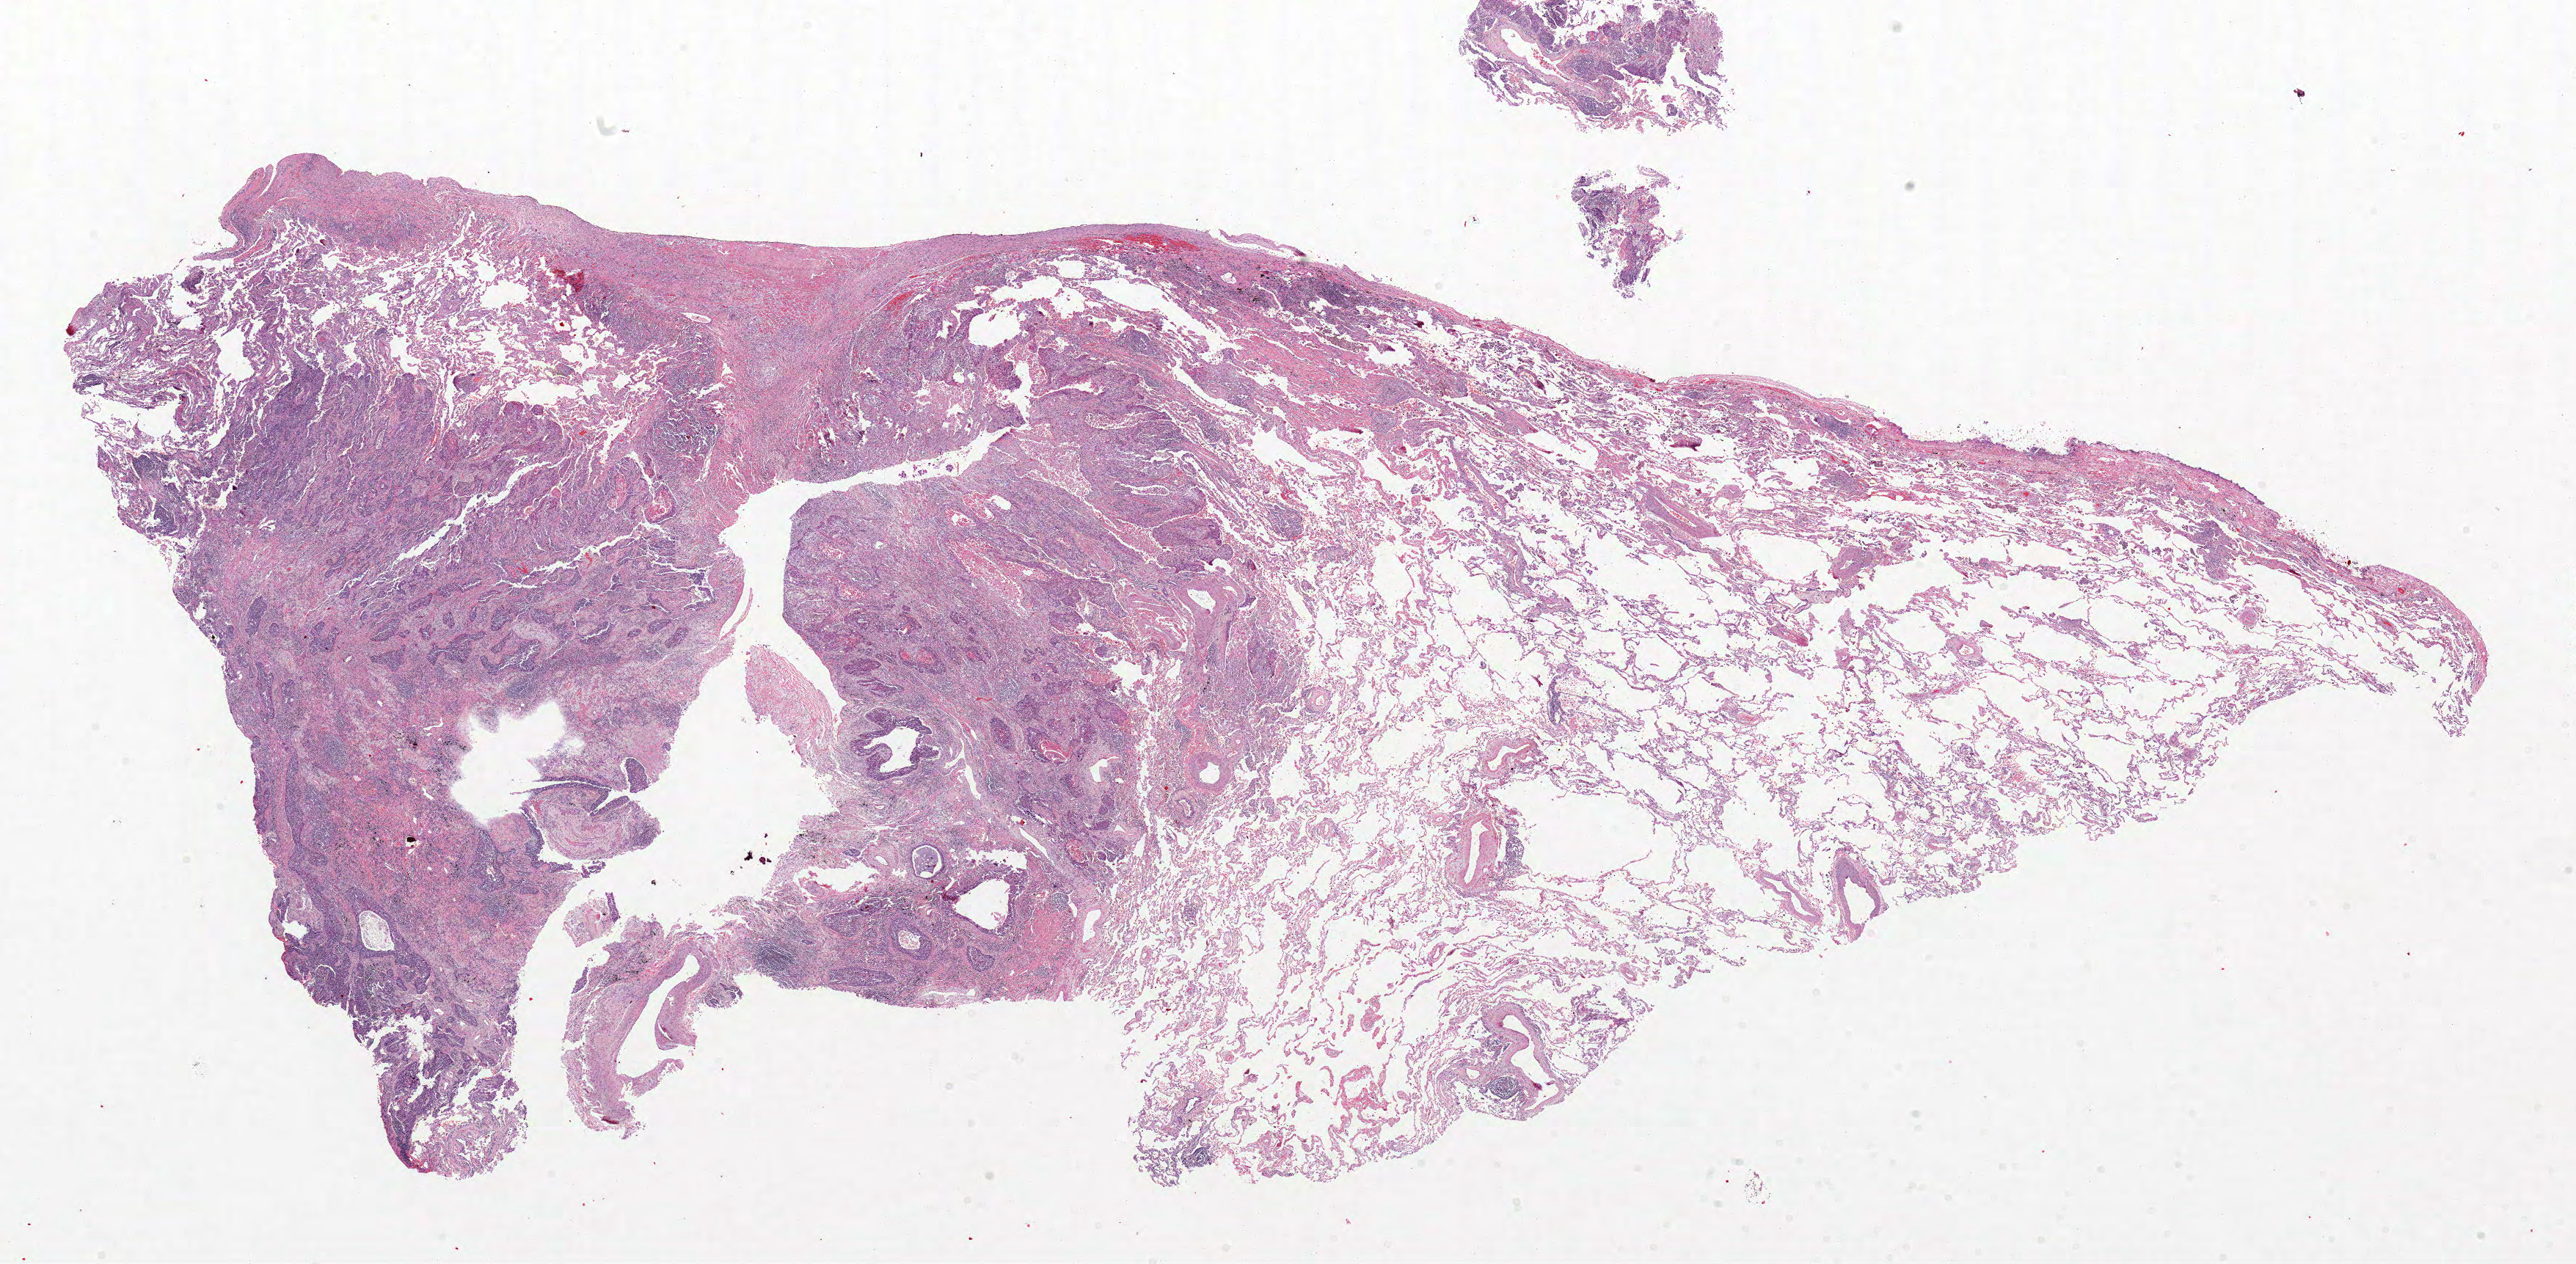
Whole-slide histology image, H&E-stained, shown as a low-resolution overview of the whole scanned area (about 28.3 x 13.9 mm, slide scanned at 20x). FFPE section. Sample: primary tumour, lung. Male, age 76 years at initial diagnosis.
AJCC pathologic stage: IB (7th edition). Laterality: right. Diagnosis: Squamous cell carcinoma, NOS.